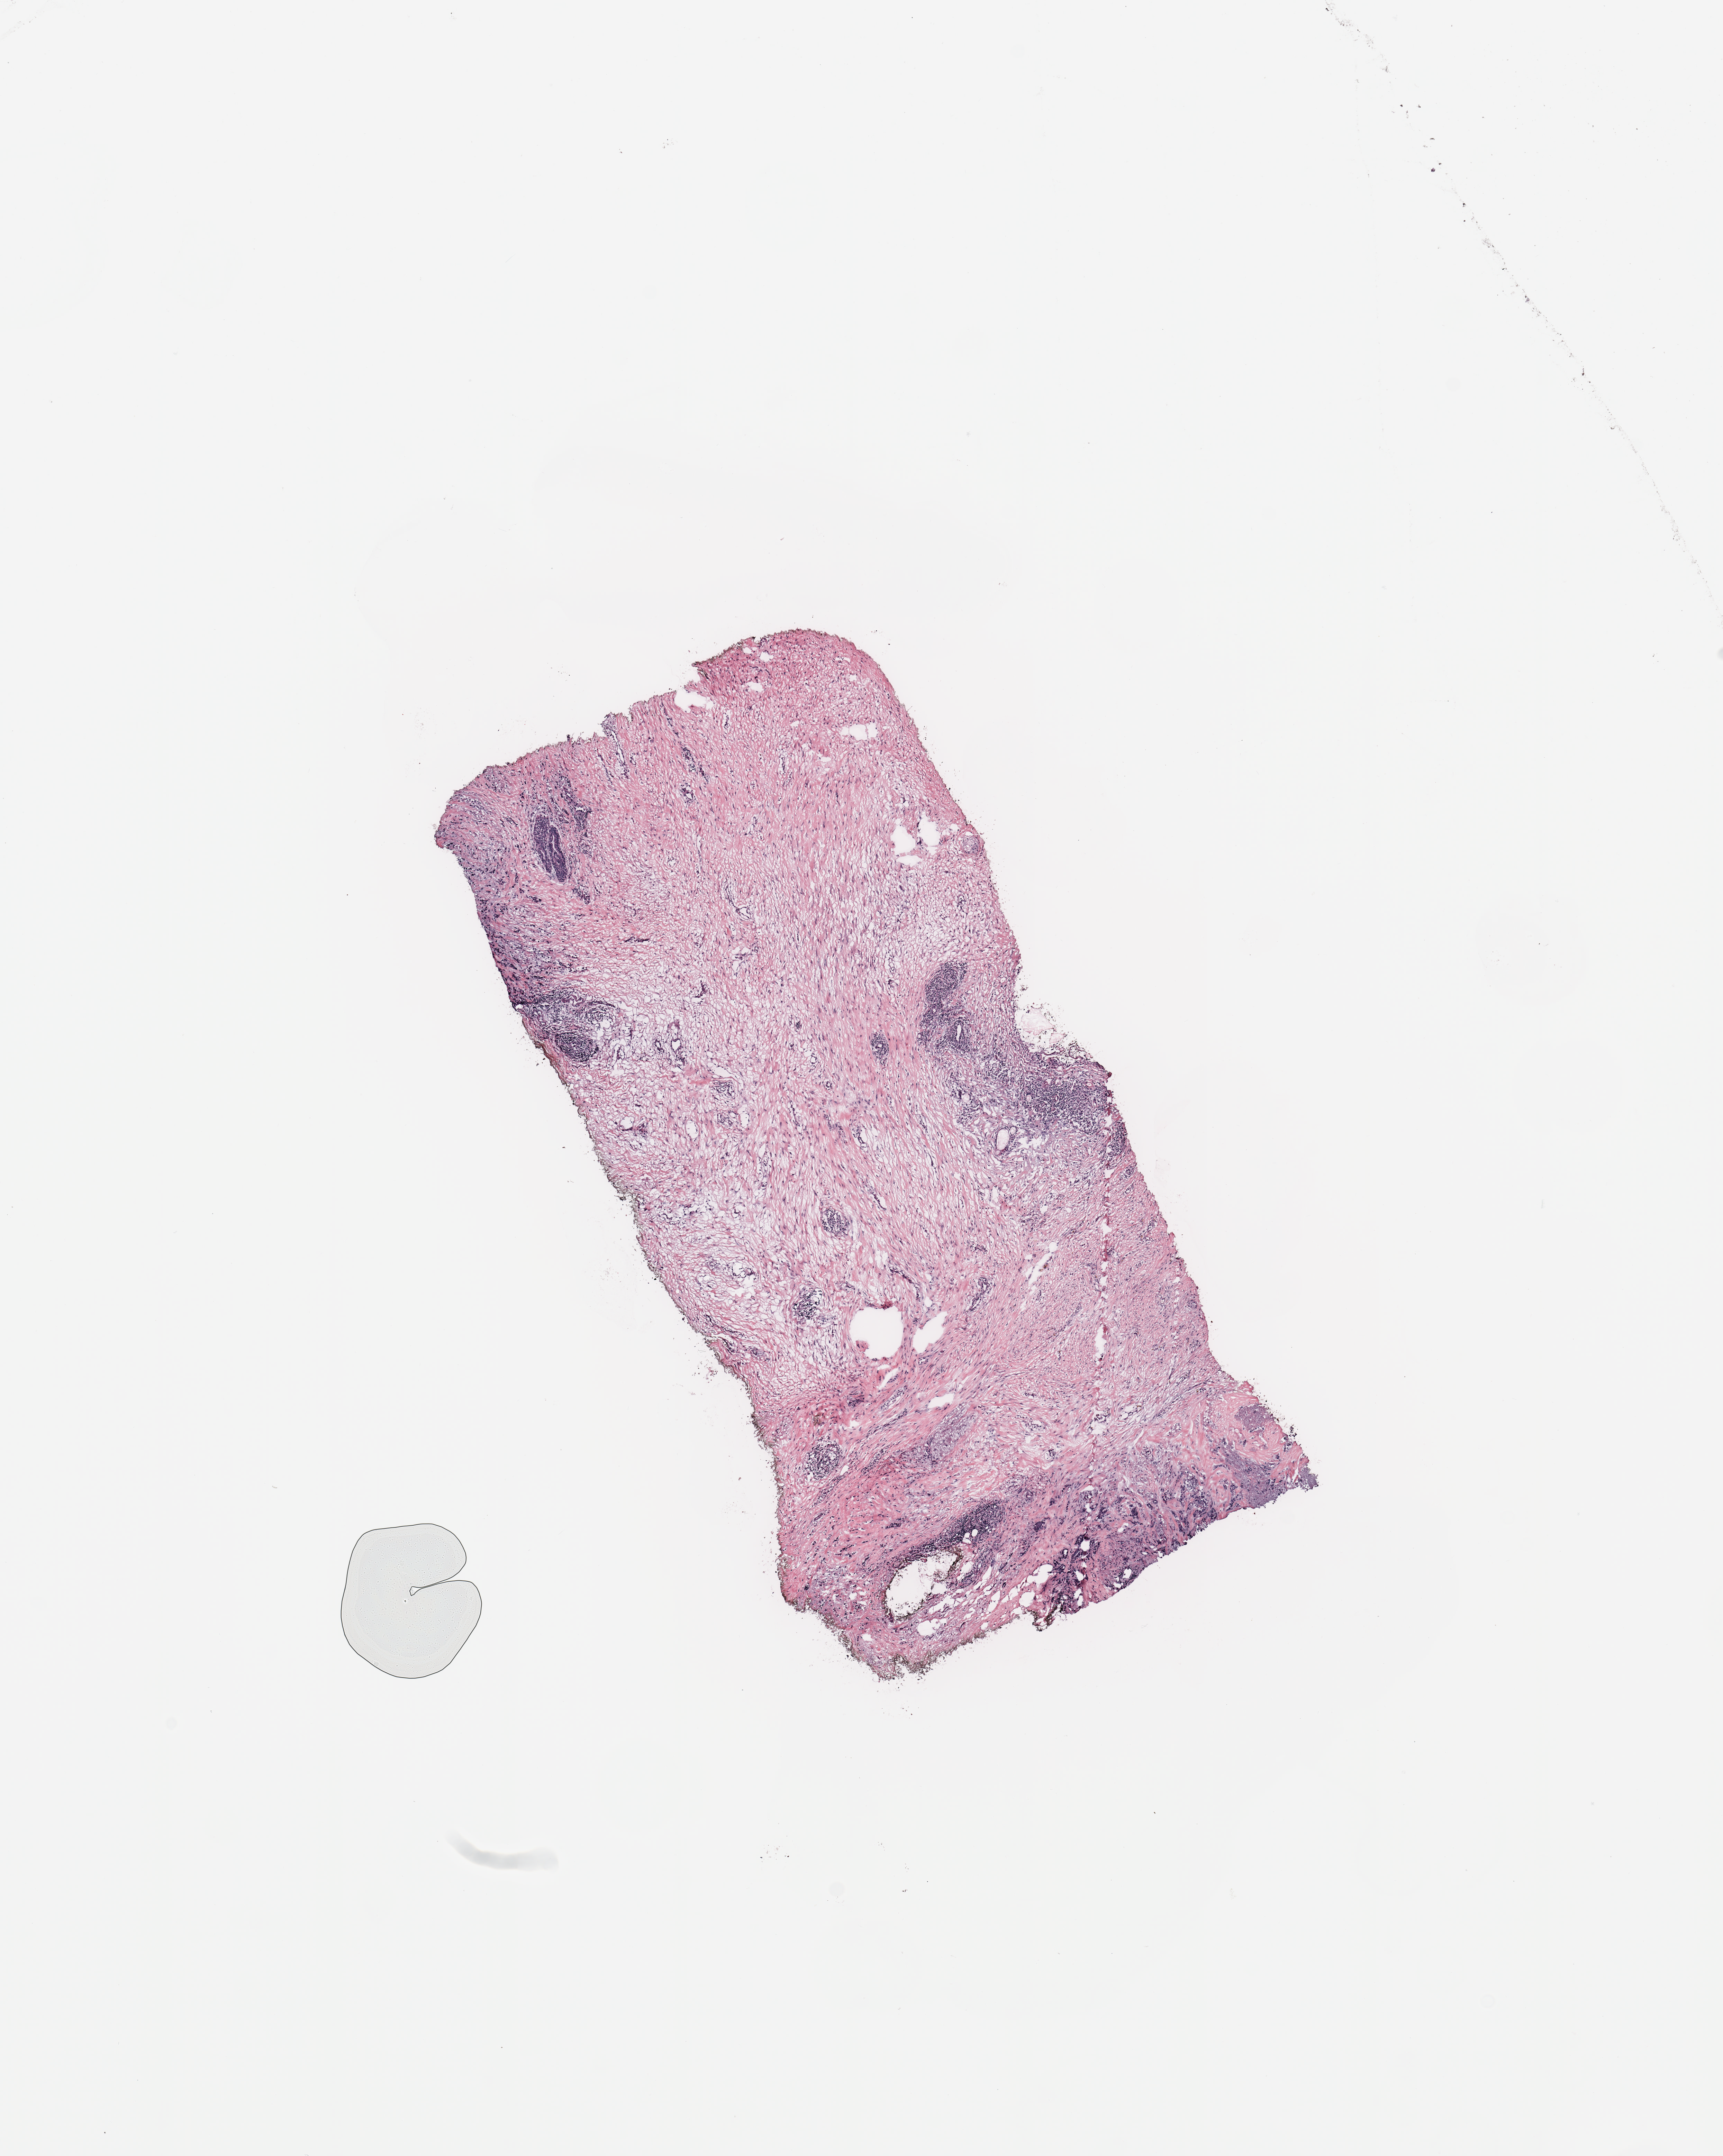
H&E-stained whole-slide image — shown as a low-resolution overview of the whole scanned area (about 9.8 x 12.3 mm, from a 20x scan); breast, tissue type not recorded.
Patient diagnosis (cohort enrolment): breast cancer (breast).